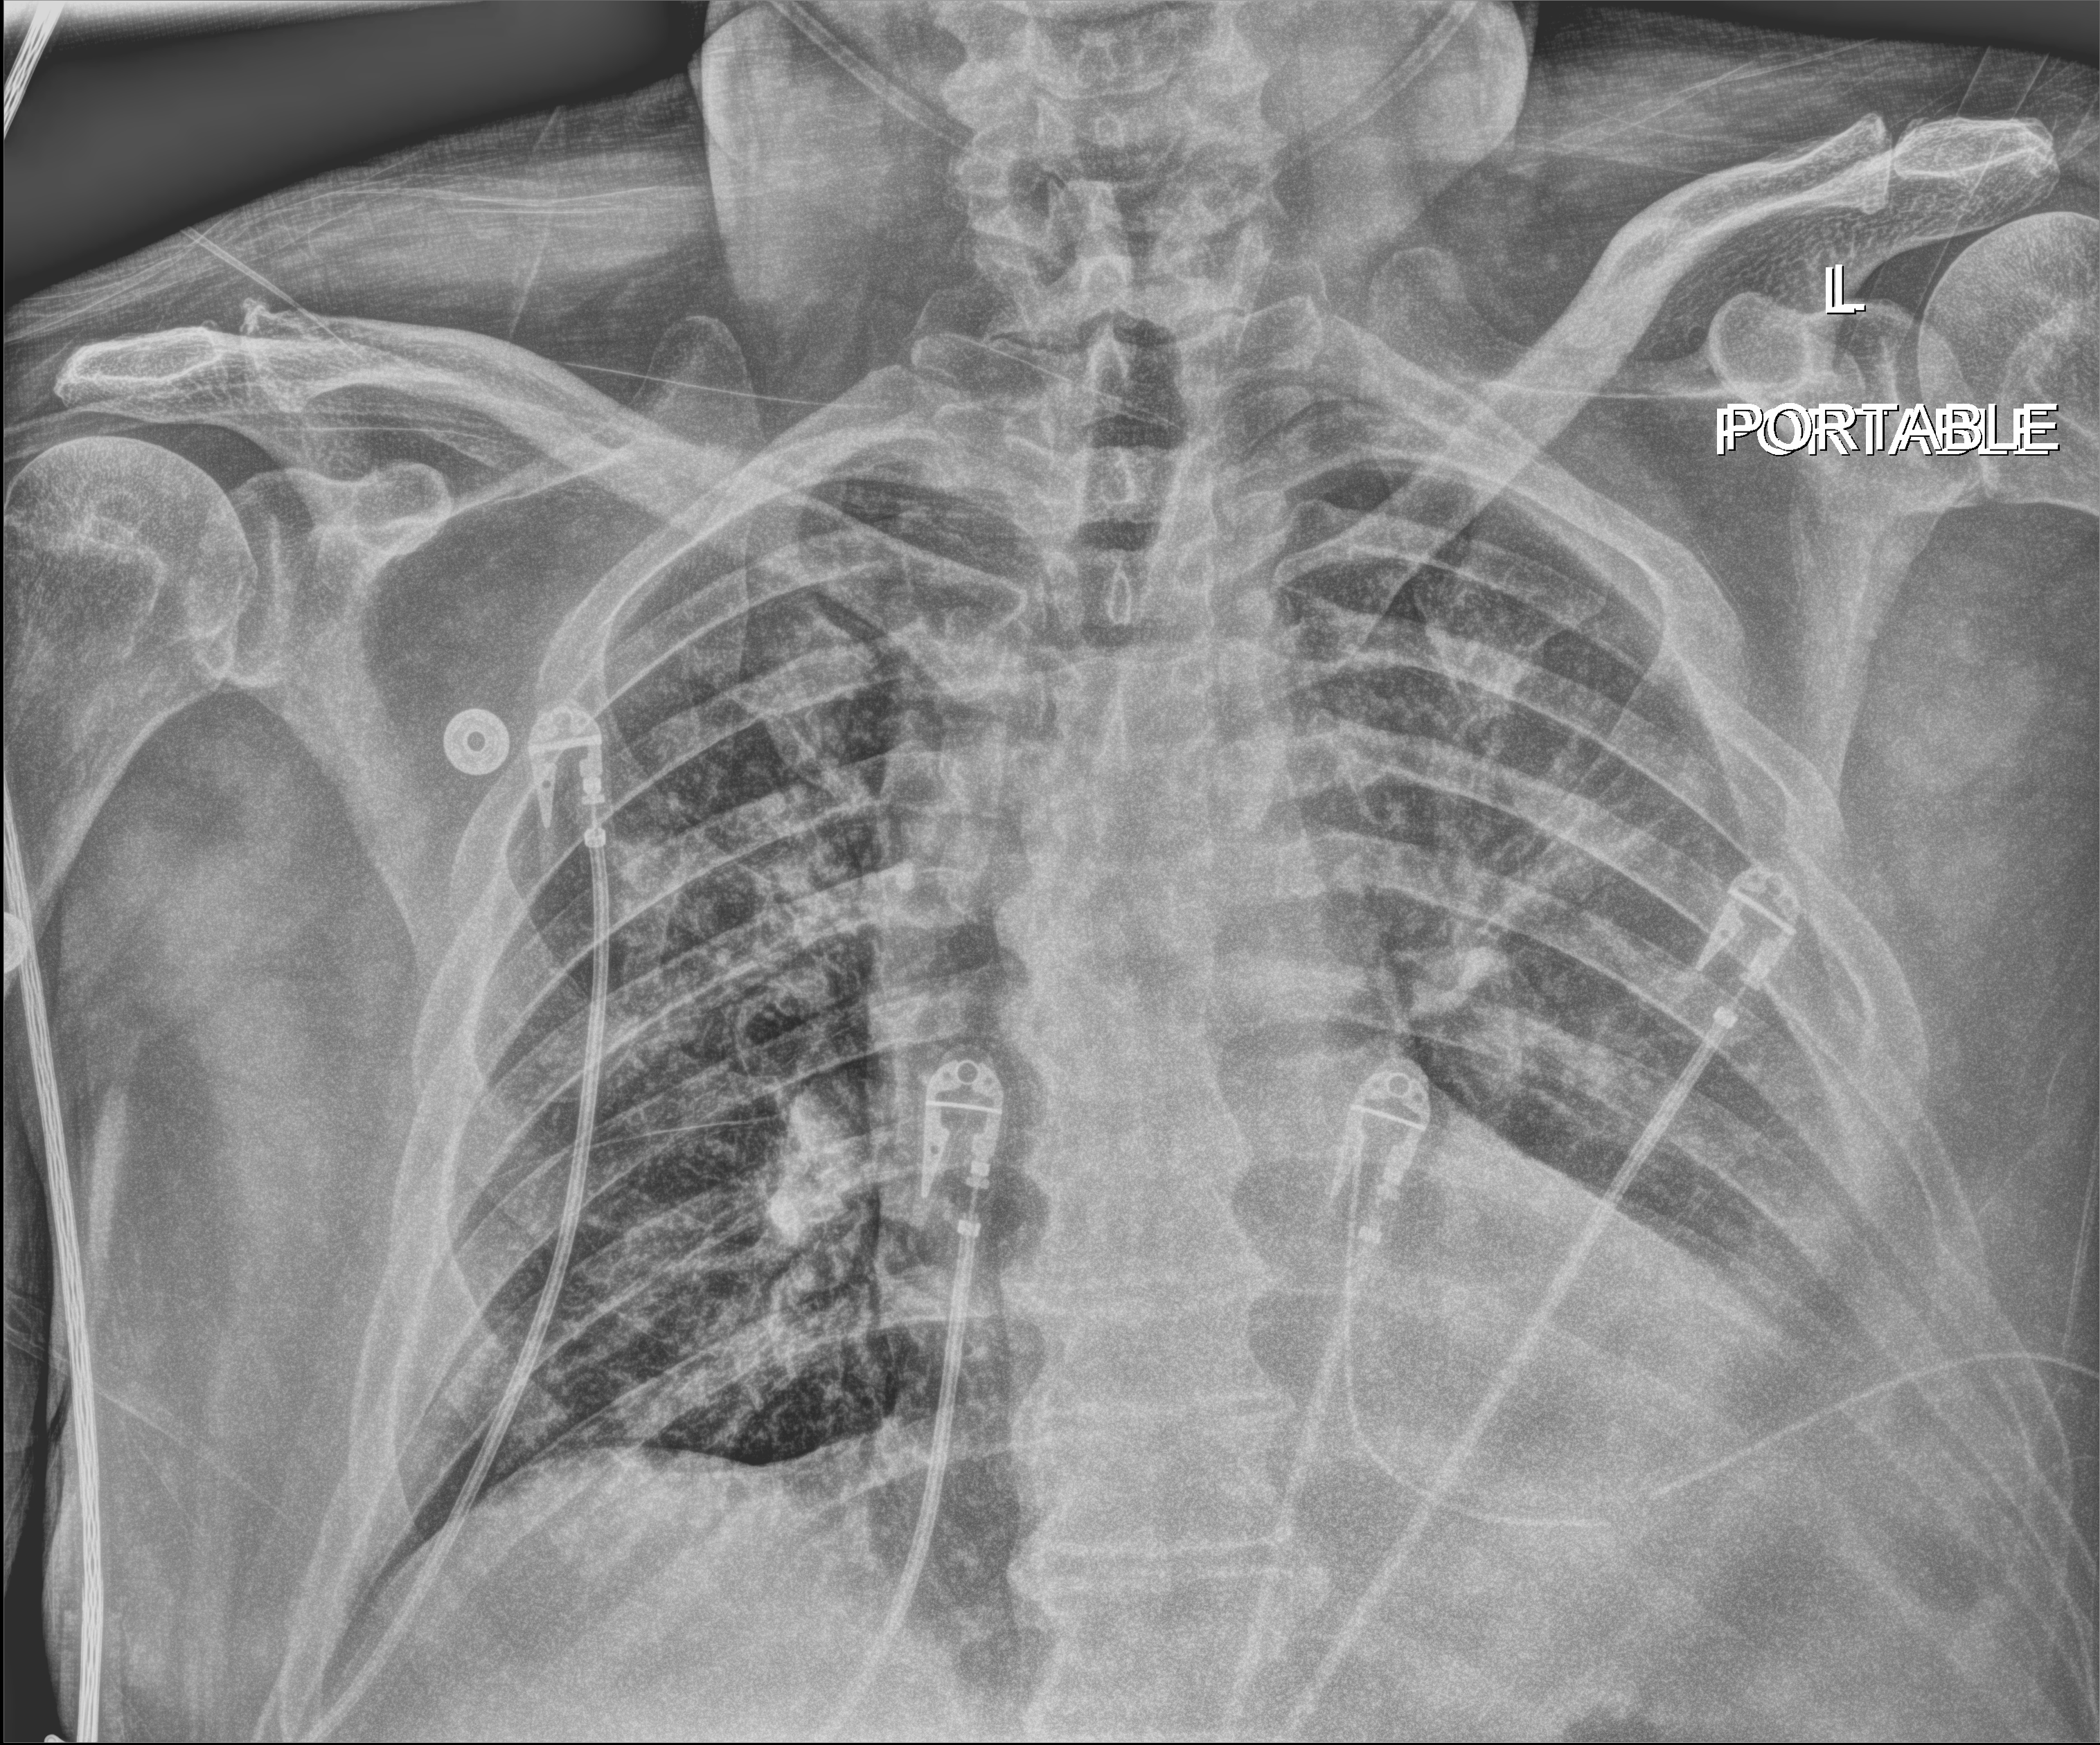
Bedside chest radiograph (digital radiography); anteroposterior (AP) projection. Male patient hospitalised with COVID-19, age 18–59 years.
From the hospital-stay record, not from the radiograph (when in the stay this image was taken is not recorded): admitted to intensive care during this hospital stay: no; length of hospital stay: 10 days; mechanically ventilated during this hospital stay: no.